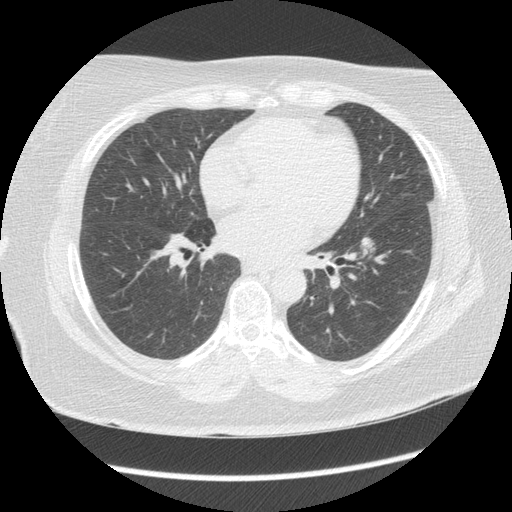
Low-dose screening chest CT, one axial slice. Slice 65 of 144 in the series (ordered by position). 120 kVp. Lung window (W 1500 / L -600 HU). 2.5 mm slice thickness. 512 × 512 image matrix.
Annotated regions visible in this slice (outlined manually by an expert reader):
- lesion 1 (tumor, lower lobe of left lung): bounding box (x1, y1, x2, y2) in pixels: (360, 237, 376, 254)